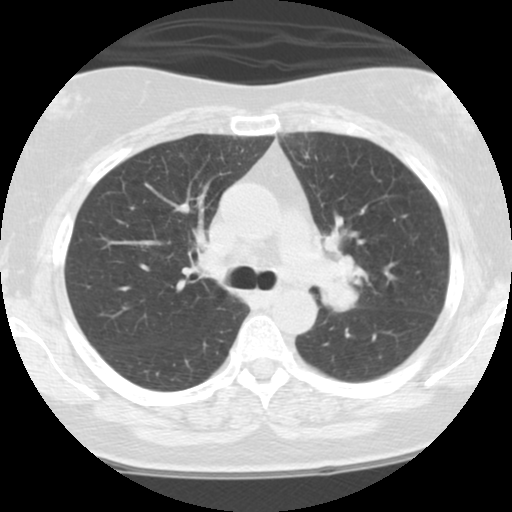
Chest CT (low-dose screening protocol), one axial image; third screening round (two years after baseline); lung window (W 1500 / L -600 HU); 2.5 mm slice thickness; 120 kVp. Female, age 59 years at enrolment.
Lesion marked by an expert reader, box from (x=285, y=213) to (x=380, y=325) px. No non-calcified nodule or mass ≥4 mm was recorded by the screening reader at this exam.